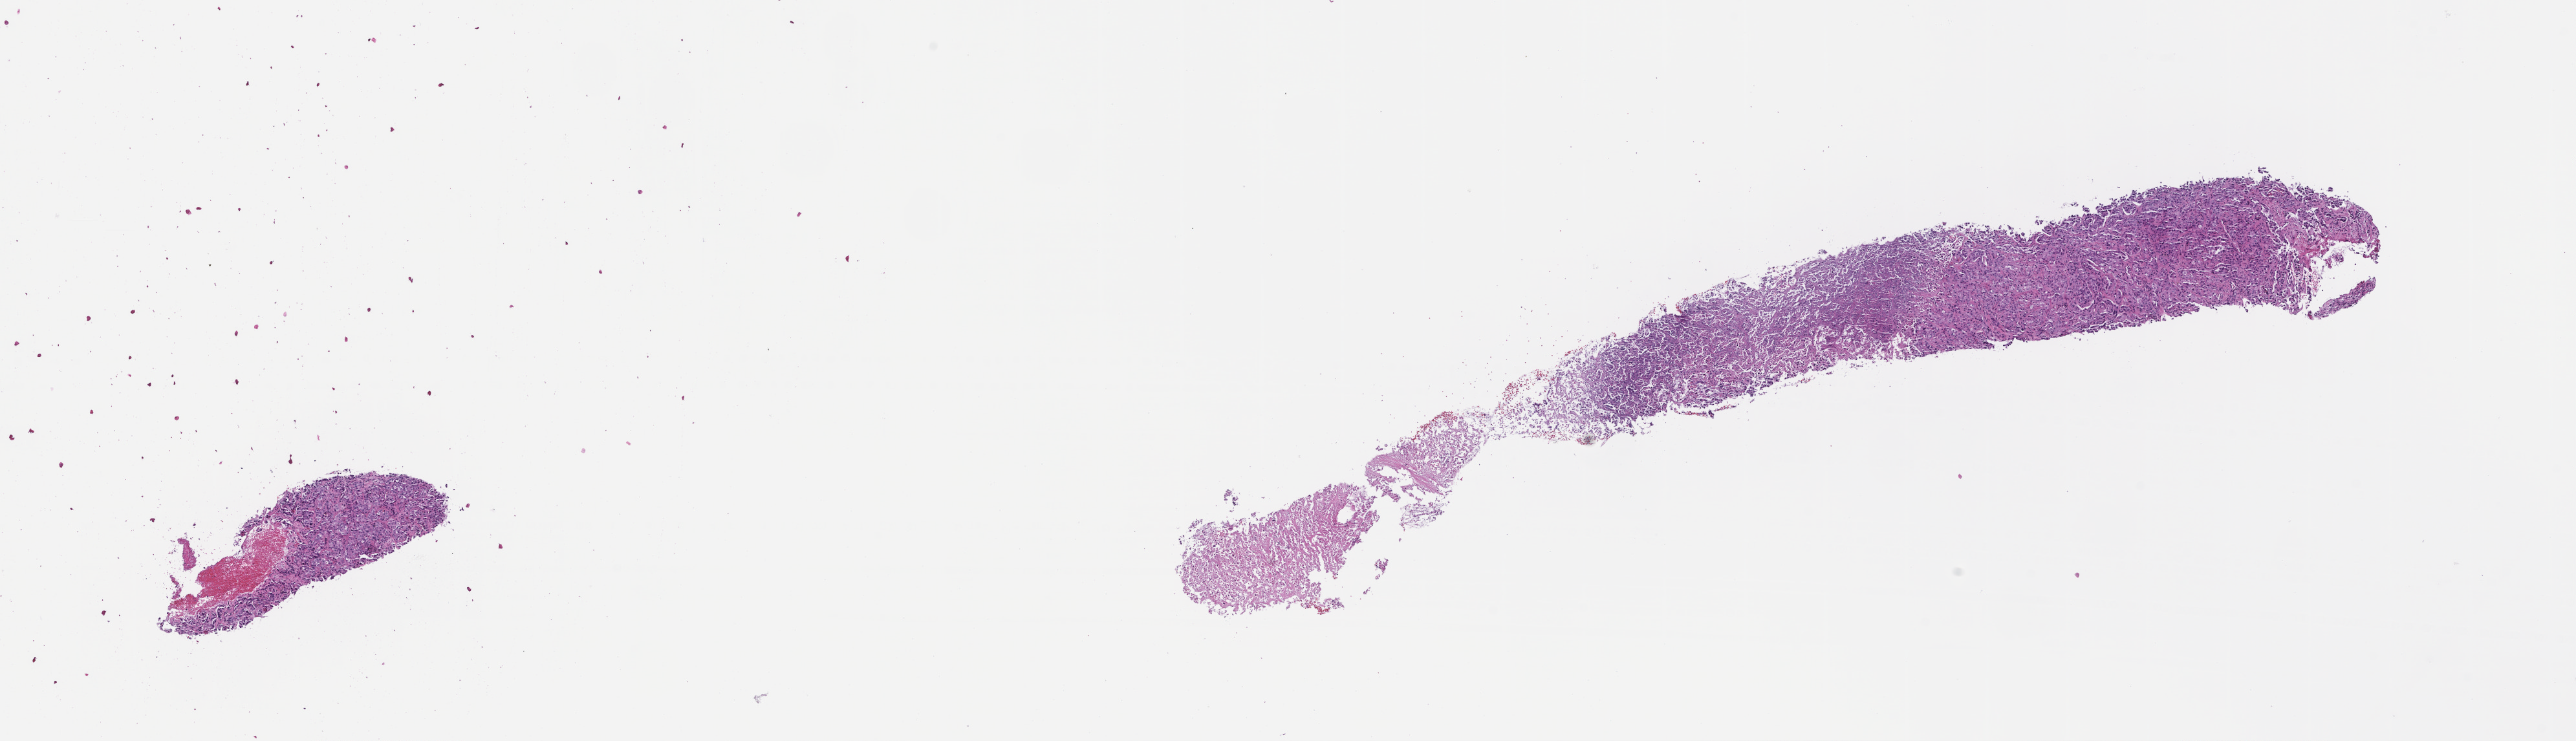
Digitized hematoxylin and eosin (H&E)-stained section, low-resolution overview of the scanned area, about 16.1 x 4.6 mm. Formalin-fixed, paraffin-embedded (FFPE) tissue. Patient: male.
This section: metastasis (sampled organ not recorded). Primary diagnosis of the patient: Non-Small Cell Lung Carcinoma.